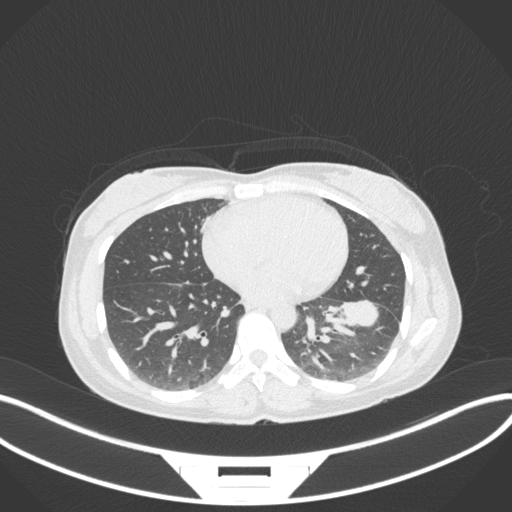
Chest CT, one axial slice; slice 146 of 361 in the series (ordered by position); reconstruction kernel B31f; 120 kVp; lung window (W 1500 / L -600 HU); 512 × 512 image matrix, field of view 400 × 400 mm. Female patient, age 41 years. From the clinical record (not read from this slice): clinical TNM (as recorded): T2a N3 M1b.
Structures marked on this image (rectangle marked by the reading radiologist):
- lung tumour (recorded histology: adenocarcinoma): box from (x=330, y=293) to (x=388, y=338) px